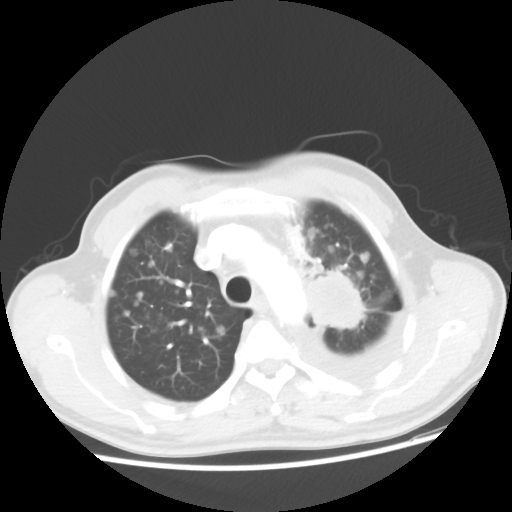
Chest CT, one axial slice; slice 37 of 48 in the series (ordered by position); reconstruction kernel STANDARD; 100 kVp; lung window (W 1500 / L -600 HU); 5 mm slice thickness; 512 × 512 image matrix, field of view 362 × 362 mm. Male patient, age 55 years. From the clinical record (not read from this slice): clinical TNM (as recorded): T2 N3 M1a.
Annotated regions visible in this slice (bounding box drawn by a radiologist):
- lung tumour (recorded histology: squamous cell carcinoma): box from (x=299, y=264) to (x=364, y=337) px